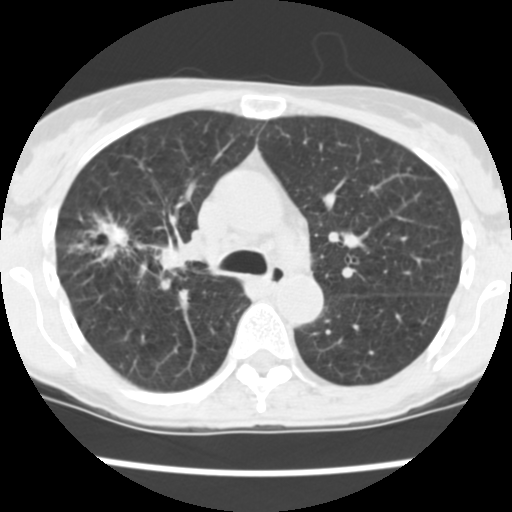
Axial slice from a low-dose chest CT screening exam, baseline annual screen, lung window (W 1500 / L -600 HU), 2.5 mm slice thickness, standard (soft-tissue) reconstruction kernel (STANDARD), slice 163 of 252 in the series, 512 × 512 image matrix. Female, age 60 years at enrolment. Current smoker at enrolment.
Lesion marked by an expert reader, bounding box [x1, y1, x2, y2] px = [82, 216, 190, 283]. The screening reader recorded 3 non-calcified nodules or masses ≥4 mm on this exam; which of them this box marks is not recorded. Official screen result: positive, change unspecified: nodule(s) >= 4 mm or enlarging nodule(s), mass(es), or other non-specific abnormalities suspicious for lung cancer. Later outcome: lung cancer diagnosed 19 days after this screen — non-small cell carcinoma, right upper lobe, stage IV (AJCC 6th edition), 26 mm at pathology.